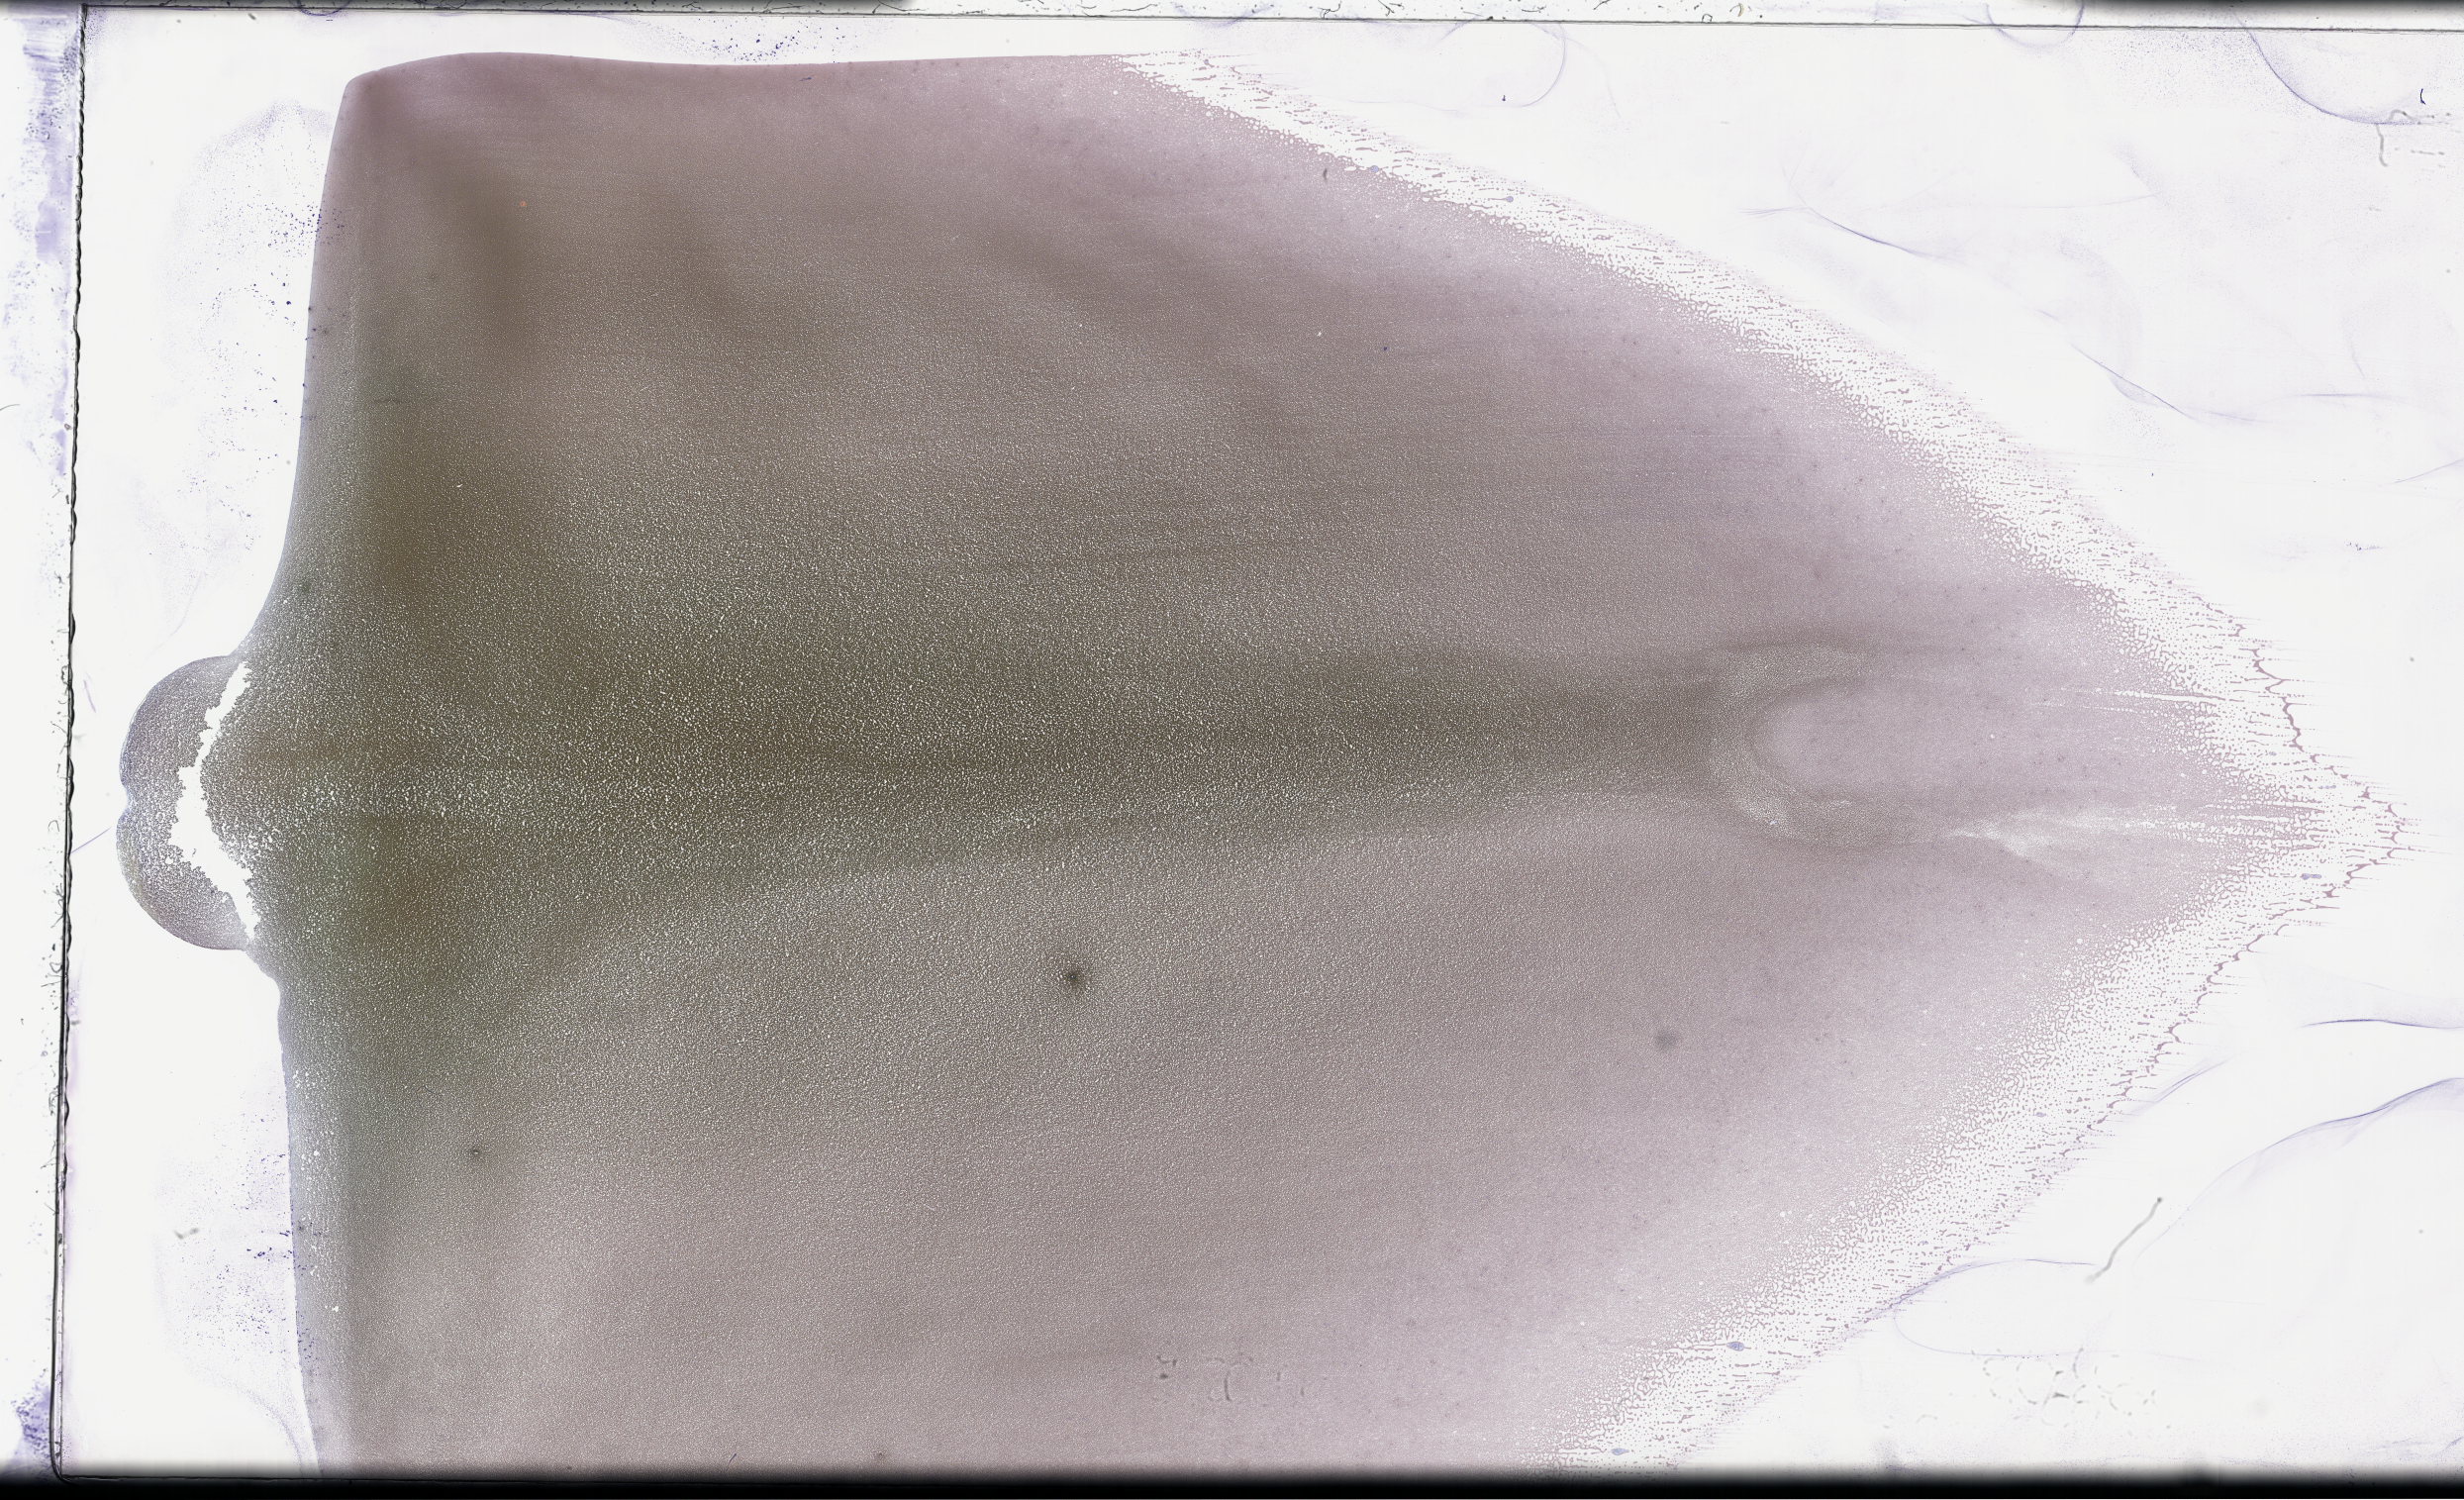
Wright-Giemsa-stained whole blood smear, whole-slide image — shown as a low-resolution overview of the whole scanned area (about 40.2 x 24.5 mm); specimen time point: collected on treatment. Patient sex: male.
Patient diagnosis: Plasma Cell Myeloma.